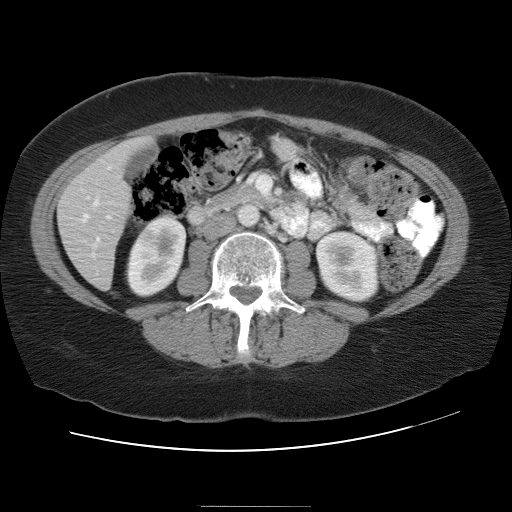
Contrast-enhanced abdominal CT, one axial slice. Slice 10 of 30 in the series (ordered by position). Reconstruction kernel STANDARD. 120 kVp. Soft-tissue window (W 400 / L 40 HU). 512 × 512 image matrix, field of view 376 × 376 mm. Female patient, age 52 years. Case-level facts recorded for this patient, not image findings: diagnosis: colorectal cancer liver metastases, imaged before liver resection; multiple liver metastases: no; largest metastasis: 3 cm; disease in both lobes: yes.
Annotated regions visible in this slice (manually delineated by an expert):
- hepatic veins: bounding box [x1, y1, x2, y2] px = [83, 201, 98, 221]
- liver: [58, 142, 148, 288]
- portal vein (with intrahepatic branches): [86, 168, 110, 242]